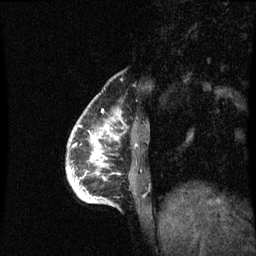
Breast MRI (dynamic contrast-enhanced), one sagittal slice; position 15 of 60 along the scan axis; dynamic contrast-enhanced series, image 2 of 3 at this slice position (ordered by acquisition); 1.5 T; TE 4.2 ms, TR 8.9 ms; 256 × 256 image matrix, field of view 200 × 200 mm. Female patient, age 35 years. From the clinical record (not read from this slice): setting: breast cancer imaged before/during neoadjuvant chemotherapy; receptor status: HR-positive, HER2-negative.
Annotated regions visible in this slice (semi-automatically segmented with operator editing):
- analysis volume of interest (the breast-tissue region the enhancement analysis was run in; not a lesion): box from (x=67, y=106) to (x=120, y=203) px
- tumour enhancement mask (voxels above the 70 % enhancement threshold inside the analysis volume of interest): (x=86, y=126)–(x=108, y=201)